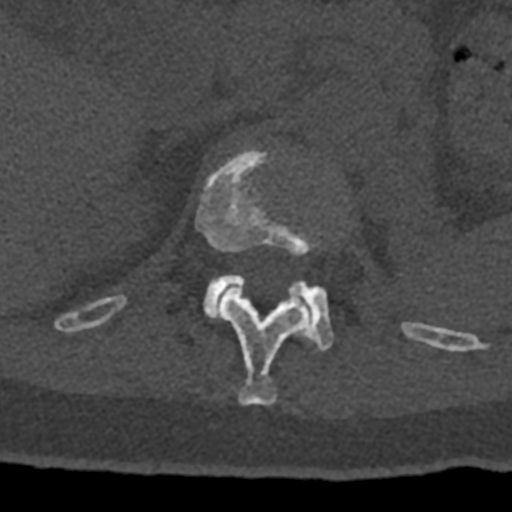
CT including the spine, one axial slice; 120 kVp; bone window (W 1800 / L 400 HU); 0.5 mm slice thickness; 512 × 512 image matrix, field of view 160 × 160 mm. Male patient, age 74 years. From the clinical record (not read from this slice): primary cancer: renal; vertebrae with lytic lesions (as recorded): T10, L1, L2, L3, L4, L5.
Structures marked on this image (semi-automatically segmented with operator editing):
- L1 vertebra: box from (x=204, y=274) to (x=334, y=350) px
- T12 vertebra: (x=70, y=148)–(x=432, y=405)